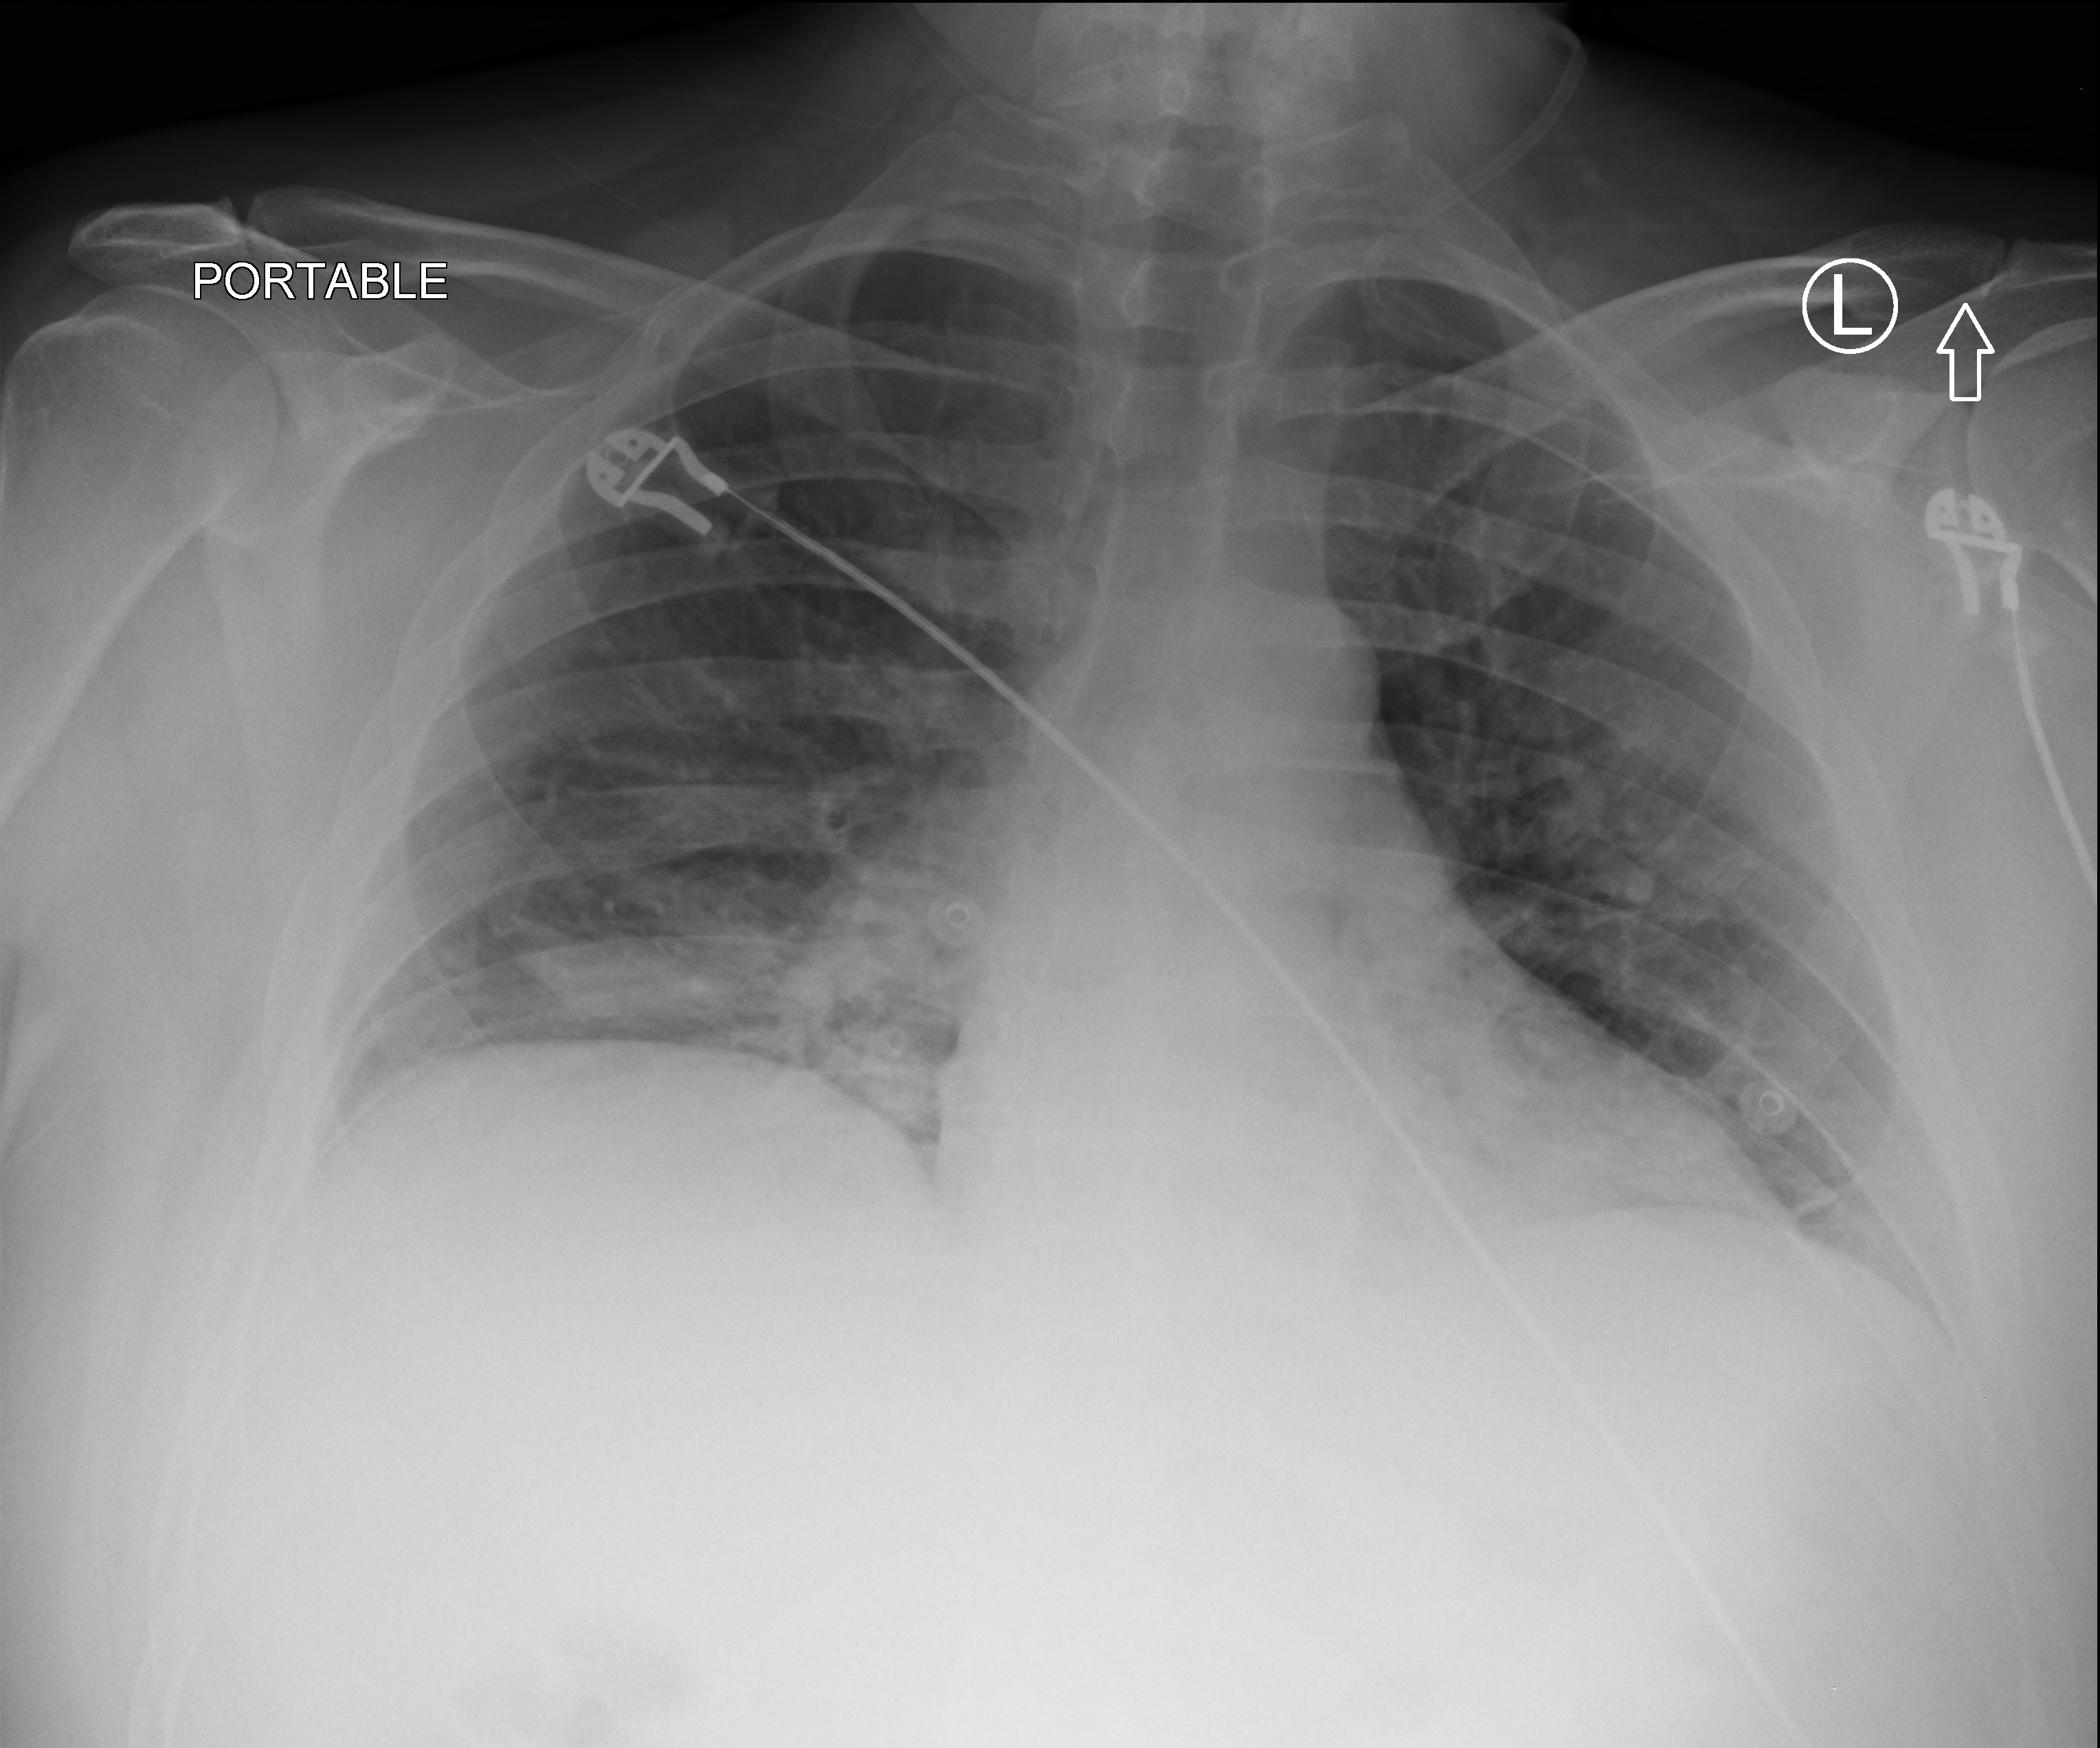
Chest X-ray (portable), anteroposterior (AP) projection. Male patient hospitalised with COVID-19, age 18–59 years.
Hospital-stay facts (about this admission, not read from this image; timing relative to this image not recorded):
- diabetes (admission record): no